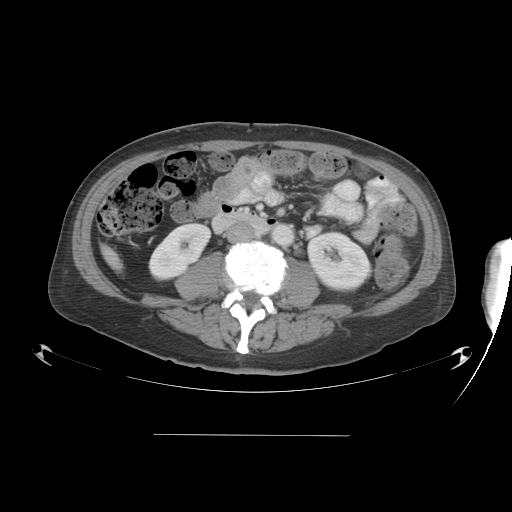
Contrast-enhanced abdominal CT, one axial slice. Slice 8 of 48 in the series (ordered by position). 120 kVp. Intravenous contrast given. Soft-tissue window (W 400 / L 40 HU). 512 × 512 image matrix. Male patient, age 65 years. Case-level facts recorded for this patient, not image findings: diagnosis: colorectal cancer liver metastases, imaged before liver resection; multiple liver metastases: yes; largest metastasis: 11 cm.
Annotated regions visible in this slice (expert manual segmentation):
- liver: box from (x=107, y=253) to (x=115, y=265) px